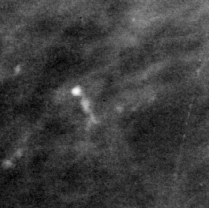
Crop from a digitized film mammogram around one marked abnormality; right breast; MLO view; BI-RADS breast density category 2 (scale 1–4).
- Finding: calcifications, morphology pleomorphic, distribution clustered; BI-RADS assessment category 4; pathology (as recorded): malignant.